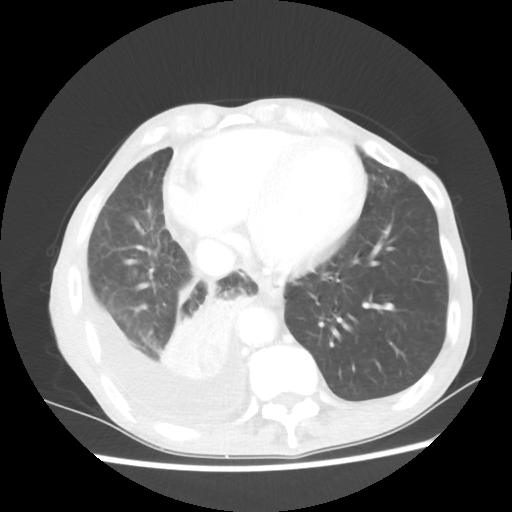
Chest CT, one axial slice. Position 18 of 60 along the scan axis. Reconstruction kernel STANDARD. 80 kVp. Lung window (W 1500 / L -600 HU). 5 mm slice thickness. 512 × 512 image matrix. Male patient, age 76 years. From the clinical record (not read from this slice): clinical TNM (as recorded): T3 N3 M1a.
Structures marked on this image (rectangle marked by the reading radiologist):
- lung tumour (recorded histology: squamous cell carcinoma): bounding box (x1, y1, x2, y2) in pixels: (158, 286, 258, 385)